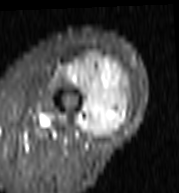
MRI of an extremity soft-tissue mass, one axial slice; slice 43 of 103 in the series (ordered by position); STIR; MR volume resampled by the dataset authors to the PET/CT grid (not the native acquisition matrix); 3.27 mm slice thickness; 179 × 193 image matrix, field of view 175 × 188 mm. Female patient. From the clinical record (not read from this slice): histological type: undifferentiated – high grade; grade: high; site of the primary tumour: left thigh.
Annotated regions visible in this slice (expert contour drawn on MRI and transferred to this co-registered scan by the dataset authors):
- gross tumour volume including surrounding oedema: bounding box <57,57,131,138> (left, top, right, bottom; pixels)
- gross tumour volume (mass): <75,57,128,138>